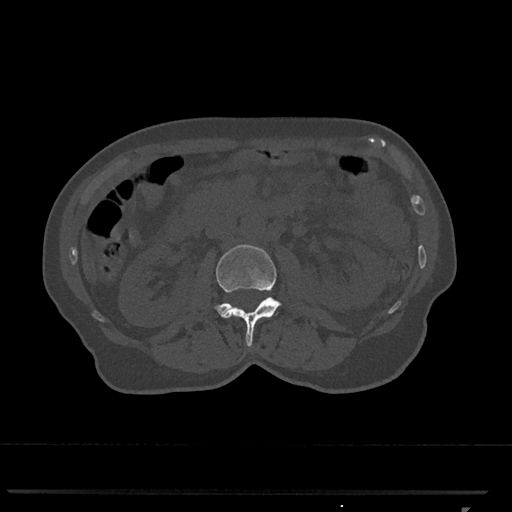
CT including the spine, one axial slice; position 333 of 793 along the scan axis; 120 kVp; bone window (W 1800 / L 400 HU); 0.5 mm slice thickness; 512 × 512 image matrix. Patient: female, 62 years. From the clinical record (not read from this slice): primary cancer: renal.
Annotated regions visible in this slice (semi-automatic segmentation, software-assisted and operator-edited):
- L2 vertebra: box from (x=214, y=245) to (x=282, y=347) px